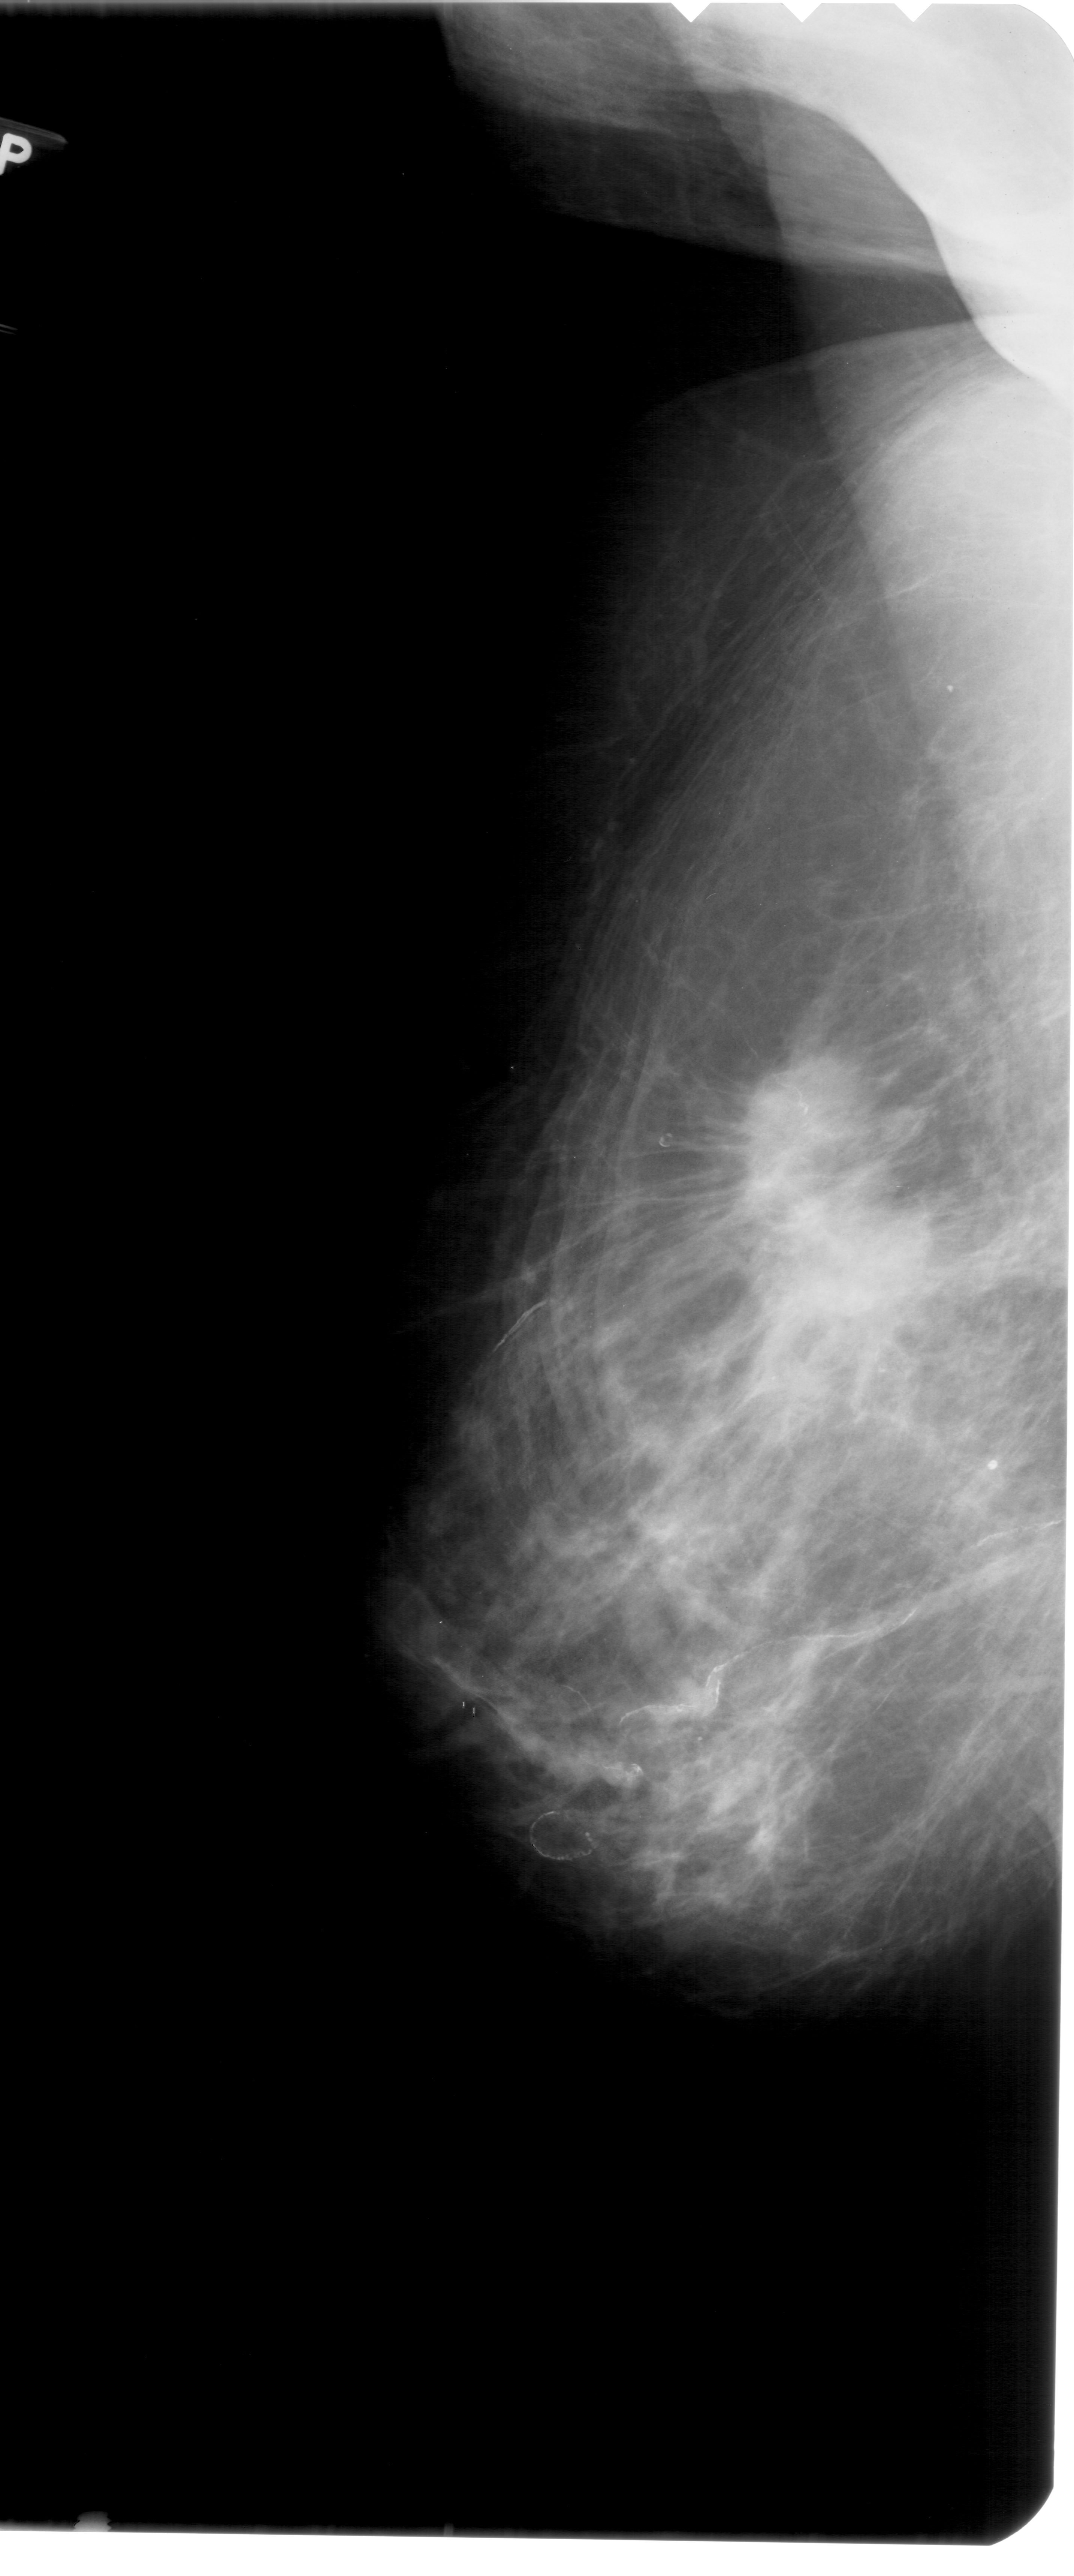
Digitized screen-film mammogram; left breast; mediolateral oblique (MLO) view; breast composition: heterogeneously dense (BI-RADS density category 3 of 4); 1074 × 2576 image matrix.
Expert-marked regions of interest on this film, with their recorded descriptors:
- mass, shape irregular, margins spiculated; BI-RADS assessment category 5; subtlety rating 5 on a 1 (subtle) to 5 (obvious) scale; pathology result (as recorded, not read from the image): malignant: bounding box [x1, y1, x2, y2] px = [640, 1032, 976, 1342]